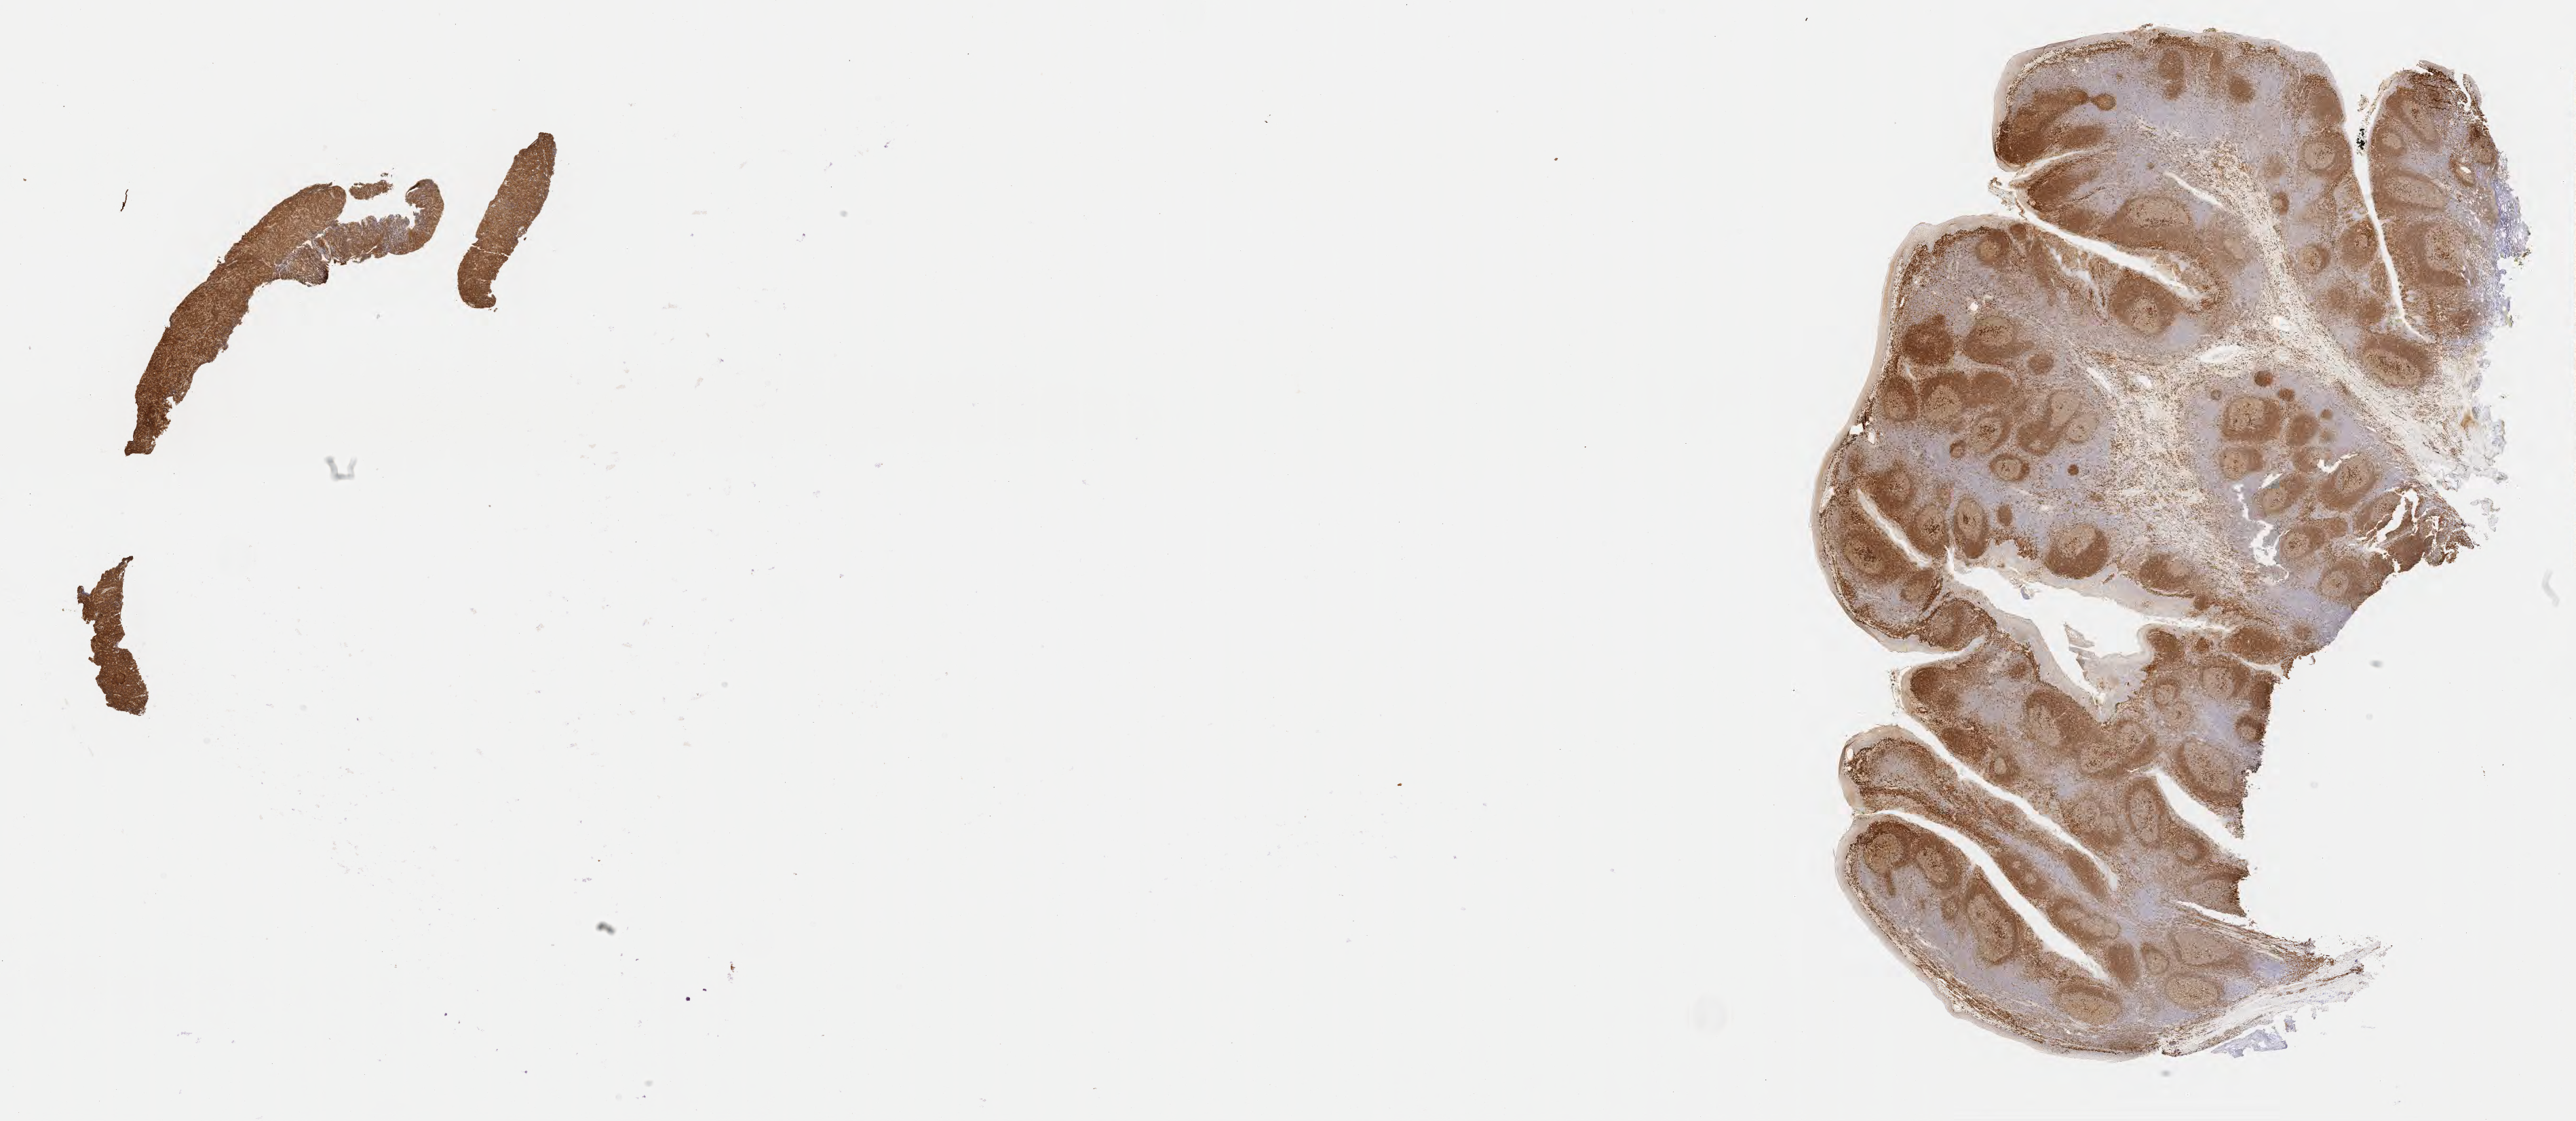
IHC for CD79a, whole-slide image, whole scanned area (about 30.7 x 13.4 mm) shown as a low-resolution overview. Tumor tissue. Patient male; aged 10.
Histologic diagnosis: Diffuse large B-cell lymphoma, NOS.